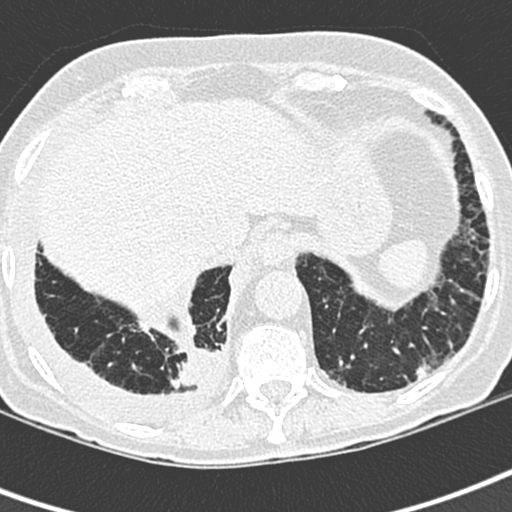
Low-dose screening chest CT, one axial slice. Slice 64 of 220 in the series (ordered by position). Lung window (W 1500 / L -600 HU). 512 × 512 image matrix, field of view 288 × 288 mm.
Structures marked on this image (manually delineated by an expert):
- lesion 1 (tumor, lower lobe of right lung): bounding box [x1, y1, x2, y2] px = [178, 346, 219, 388]
- lesion 2 (nodule, lower lobe of left lung): [417, 364, 430, 377]